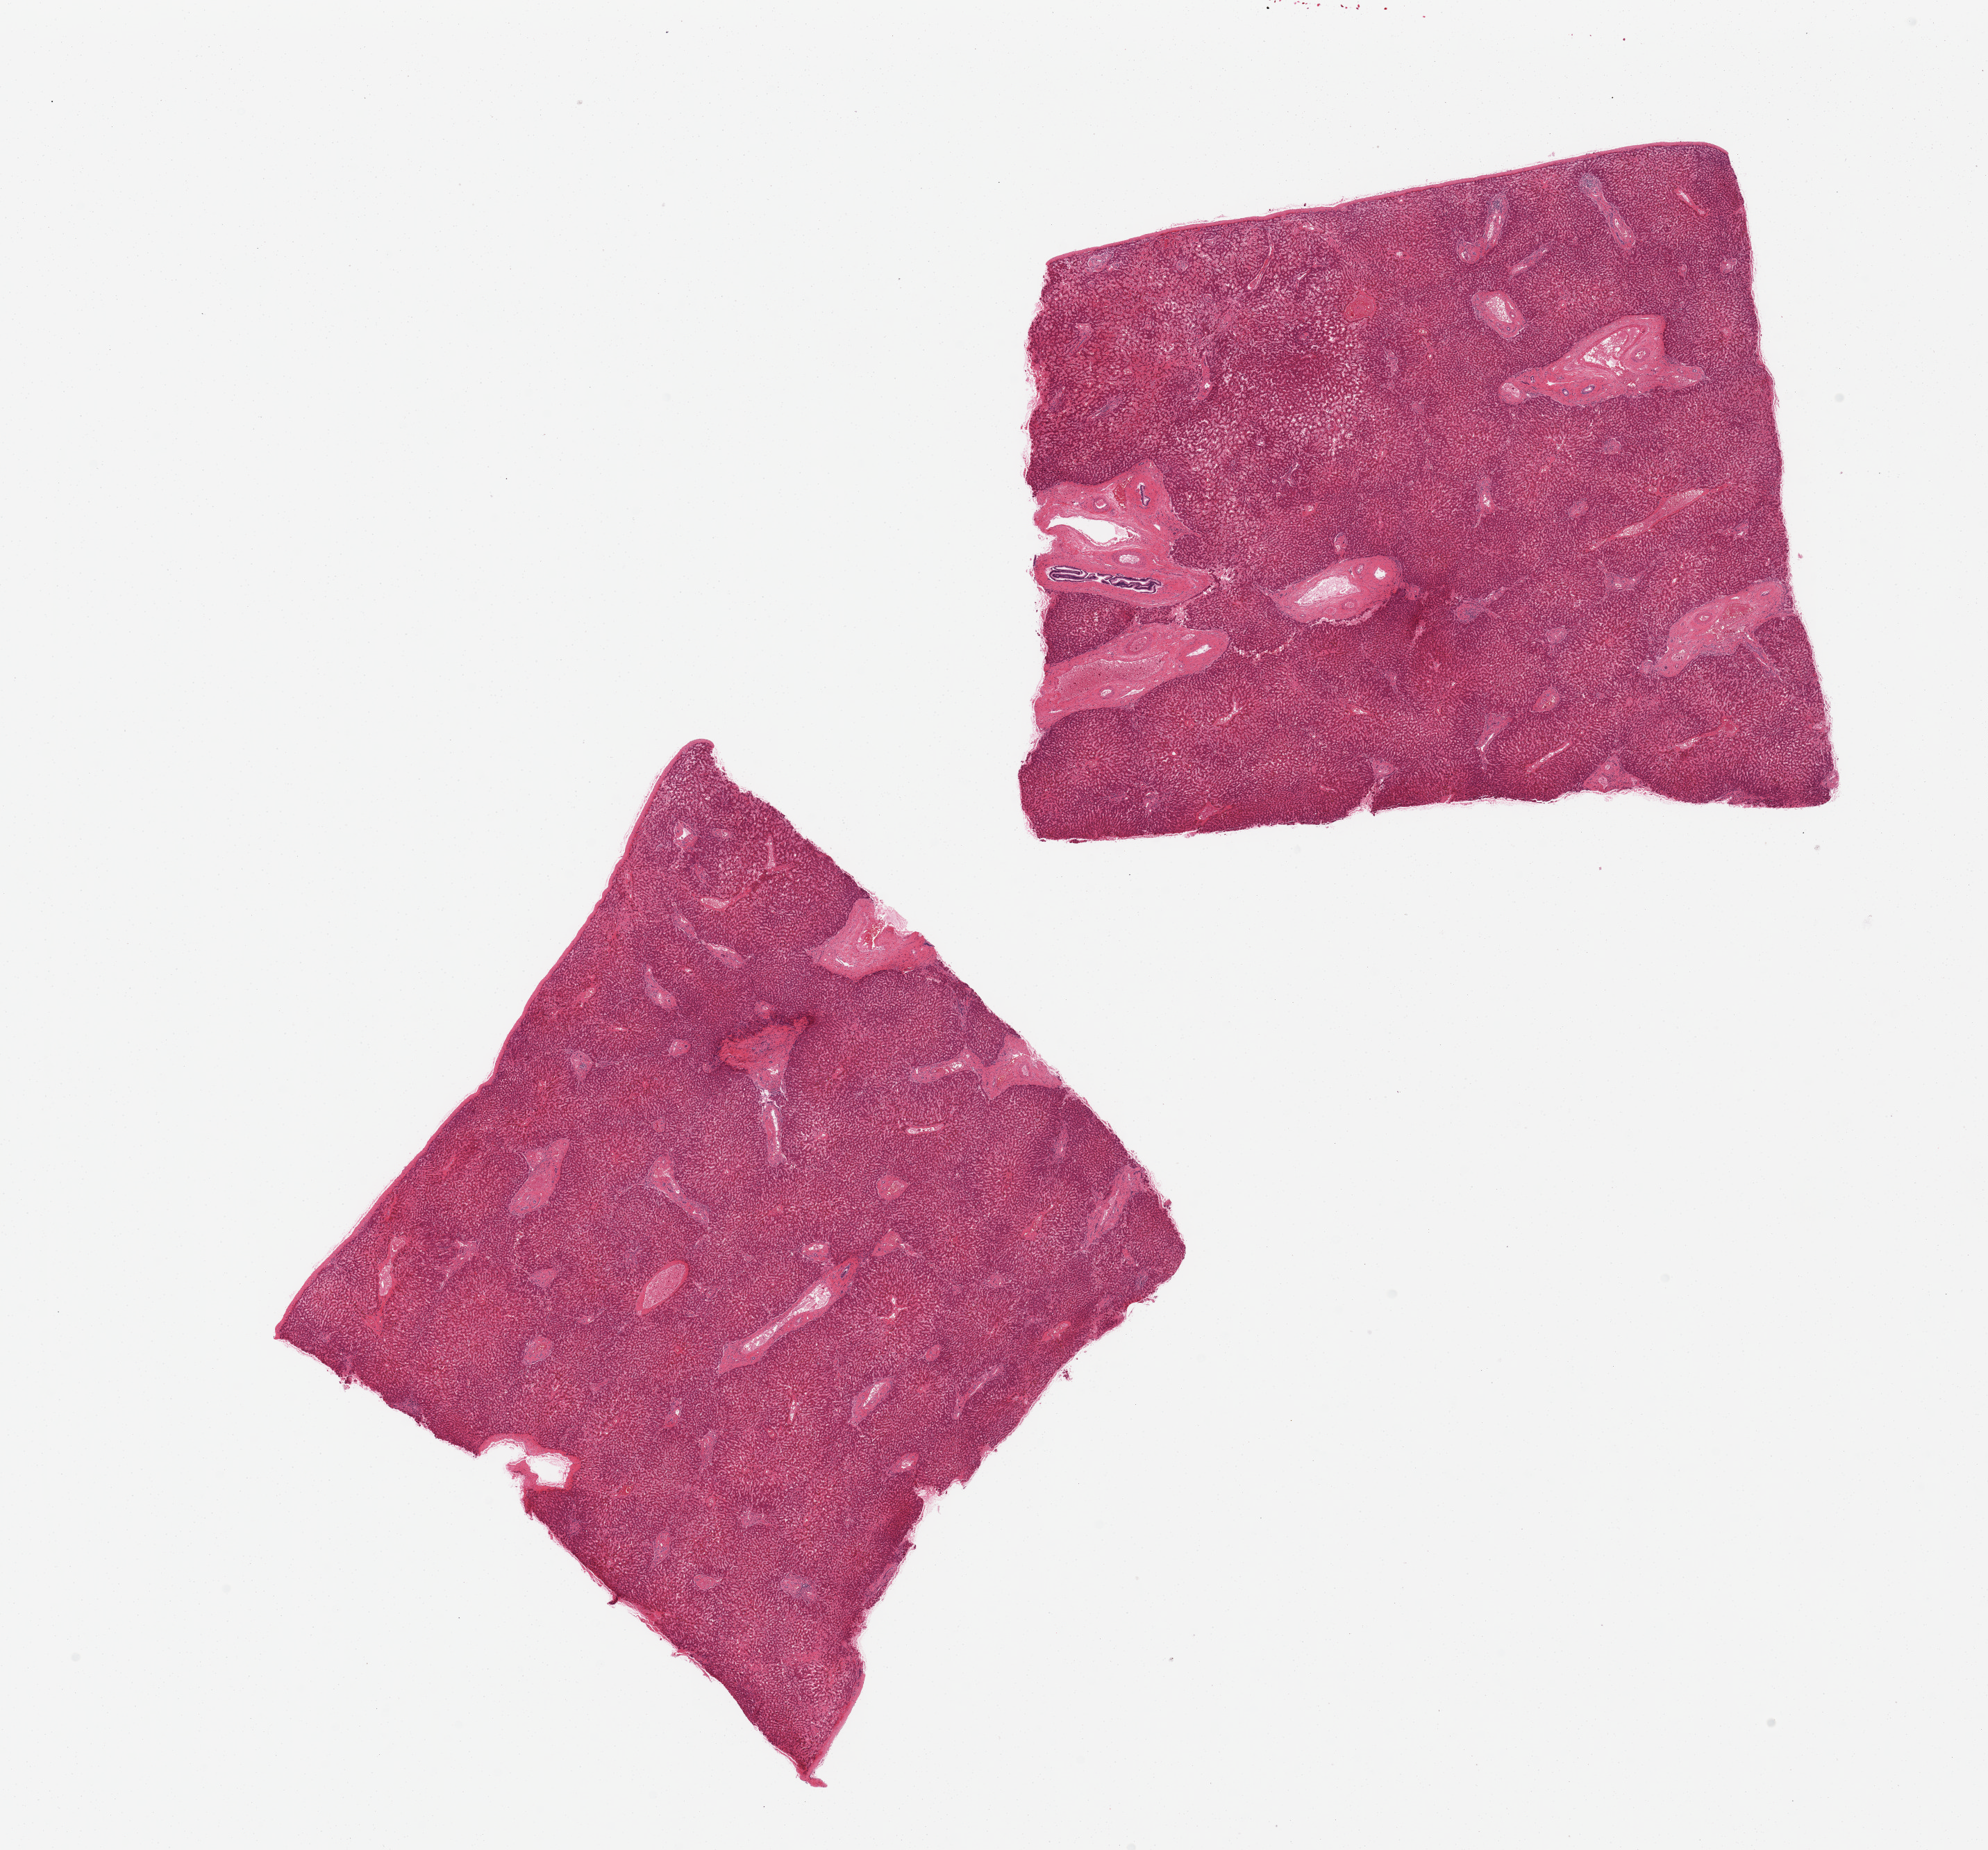
Digitized H&E-stained section, shown as a low-resolution overview of the whole scanned area (about 22.6 x 21.1 mm, slide scanned at 20x), PAXgene-fixed, paraffin-embedded tissue, section of liver (target tissue), tissue donor sample. Donor sex: female.
* review note (as recorded): 2 pieces, moderate congestion, minimal steatosis